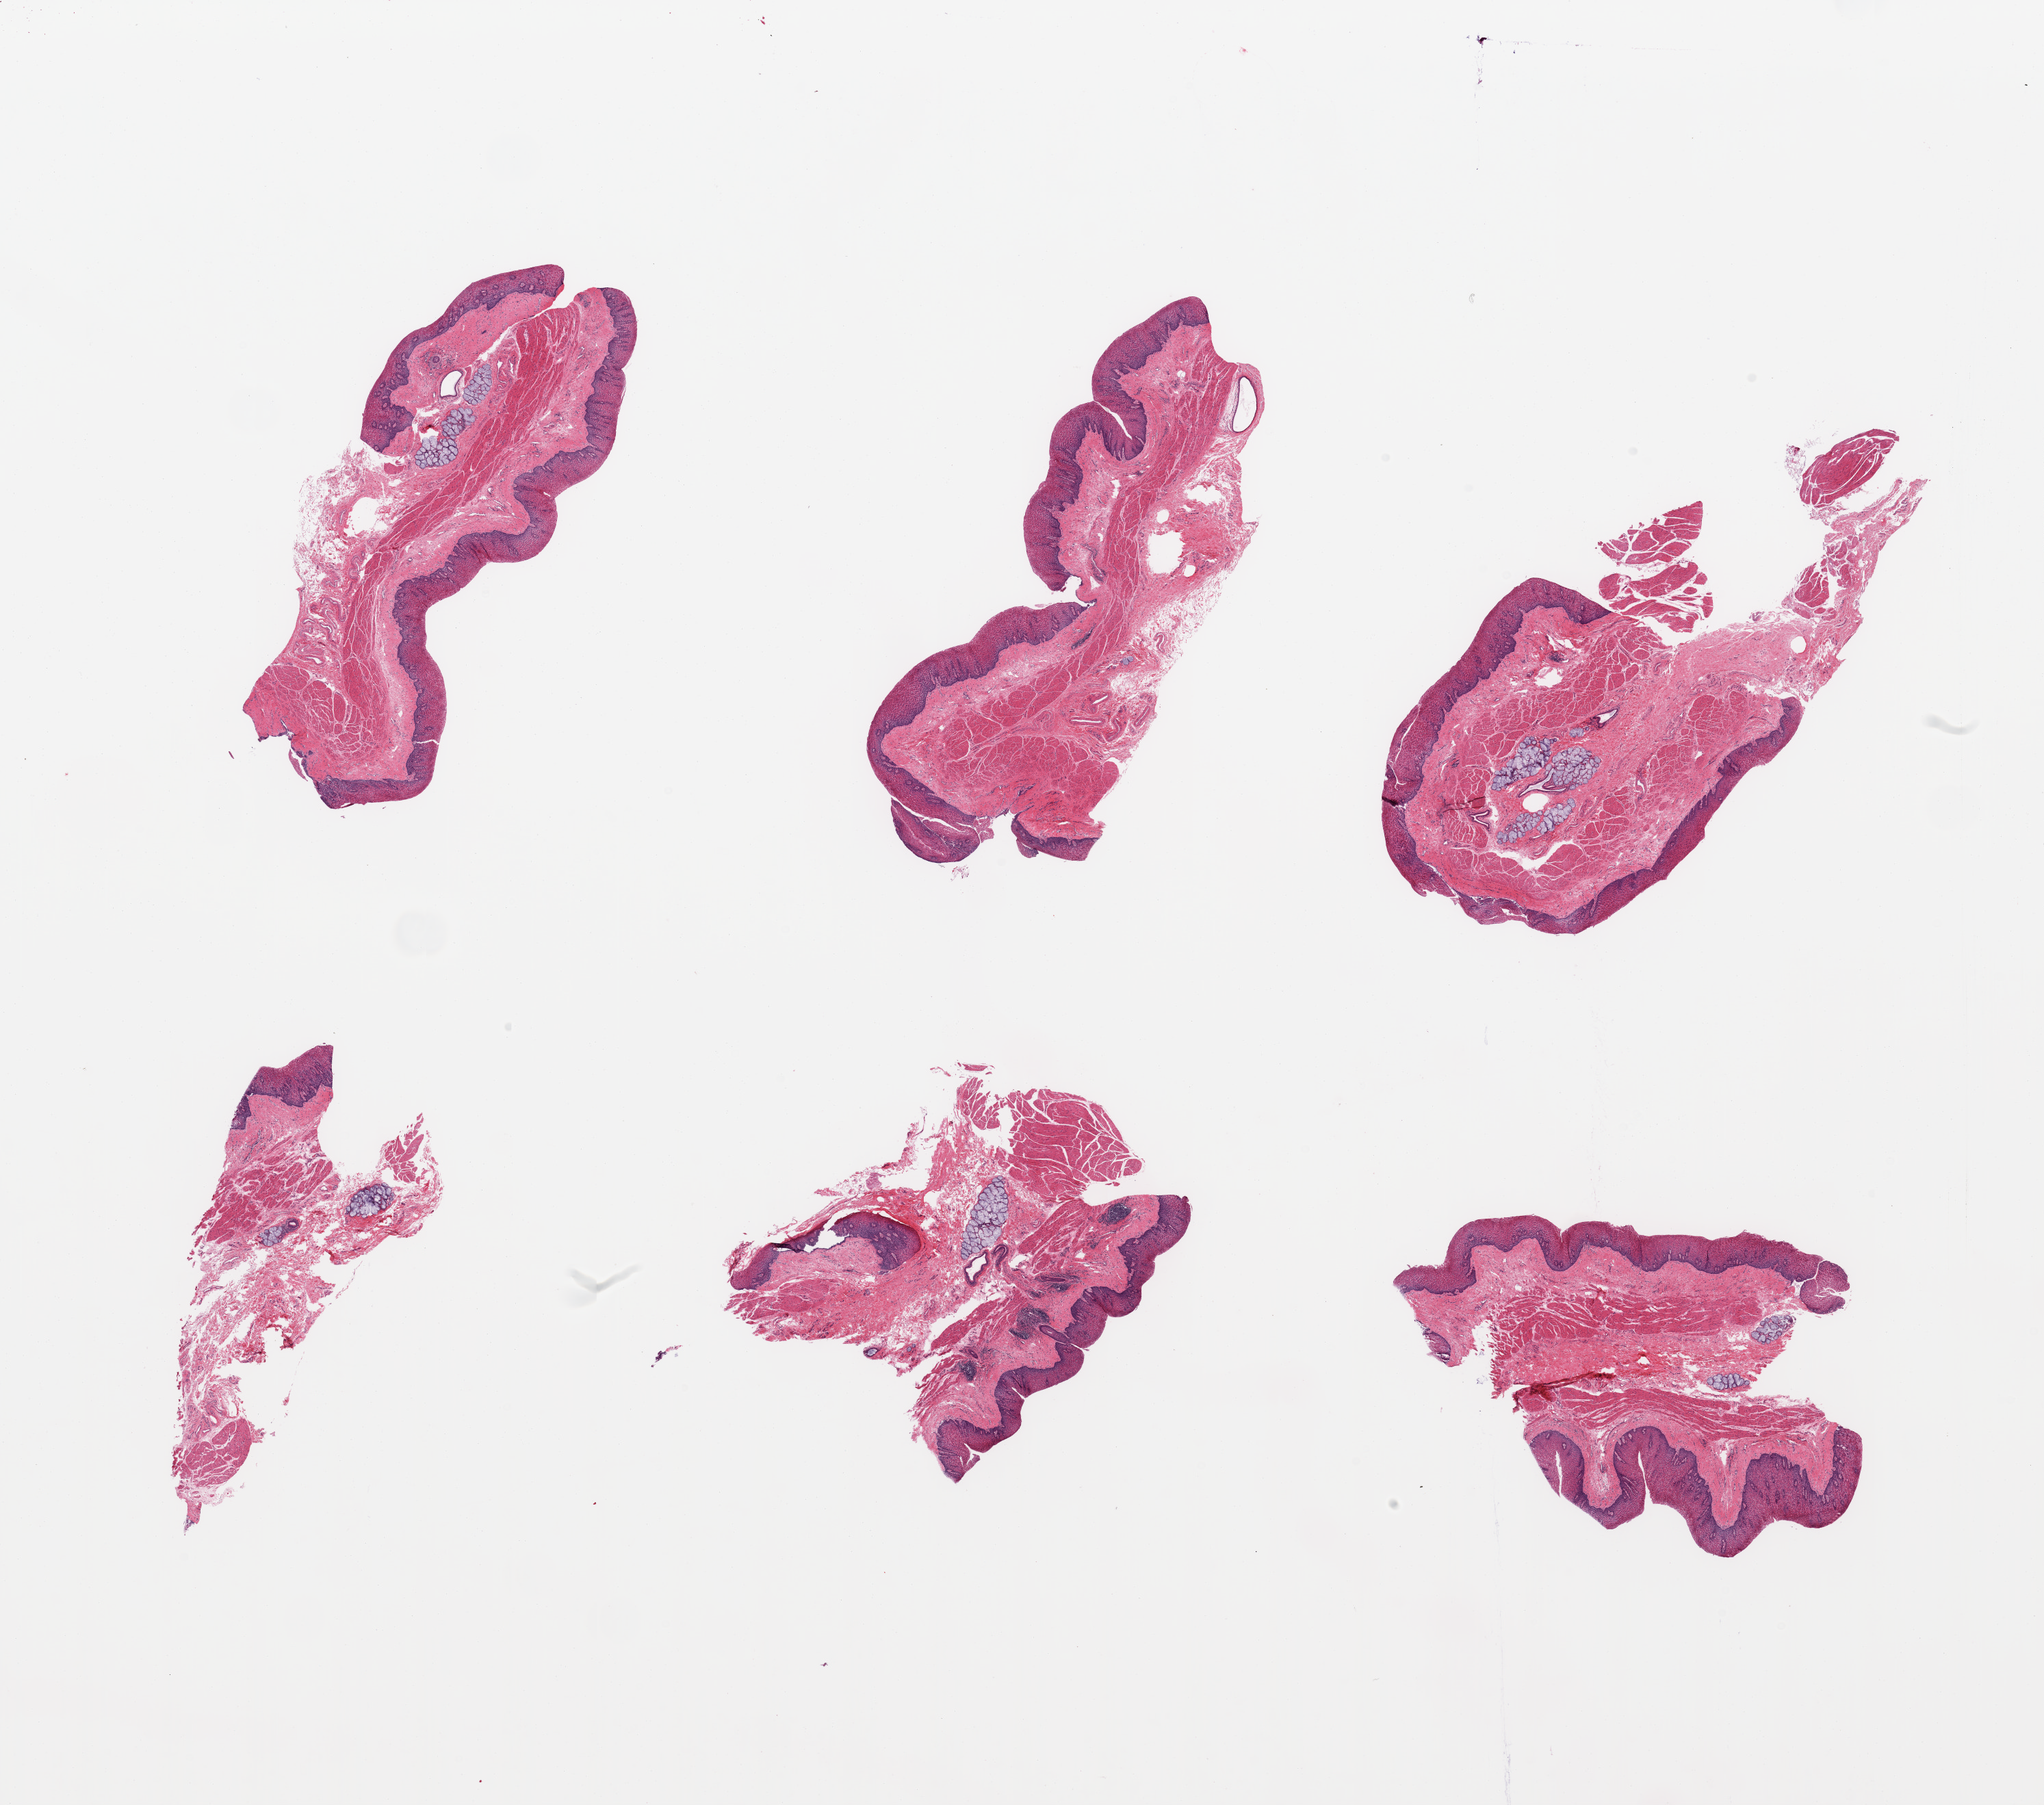
Whole-slide image, H&E stain, shown as a low-resolution overview of the whole scanned area (about 23.6 x 20.9 mm, slide scanned at 20x), PAXgene-fixed paraffin-embedded (PFPE) section, sampled site (target tissue): esophageal mucous membrane, donor tissue sample. Male donor.
• review note (as recorded): 6 pieces; 5 with submucosal mucous glands; 1 with periductal chronic inflammatory cells